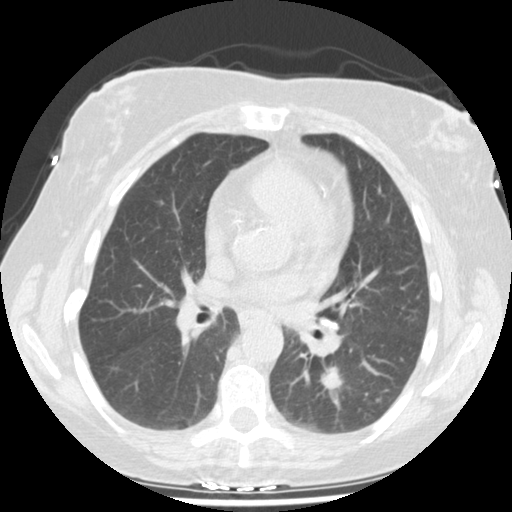
Low-dose screening chest CT, one axial slice. Position 92 of 159 along the scan axis. Reconstruction kernel STANDARD. 120 kVp. Lung window (W 1500 / L -600 HU). 512 × 512 image matrix.
Annotated regions visible in this slice (expert manual segmentation):
- lesion 1 (tumor, lower lobe of left lung): bounding box [x1, y1, x2, y2] px = [319, 366, 349, 392]